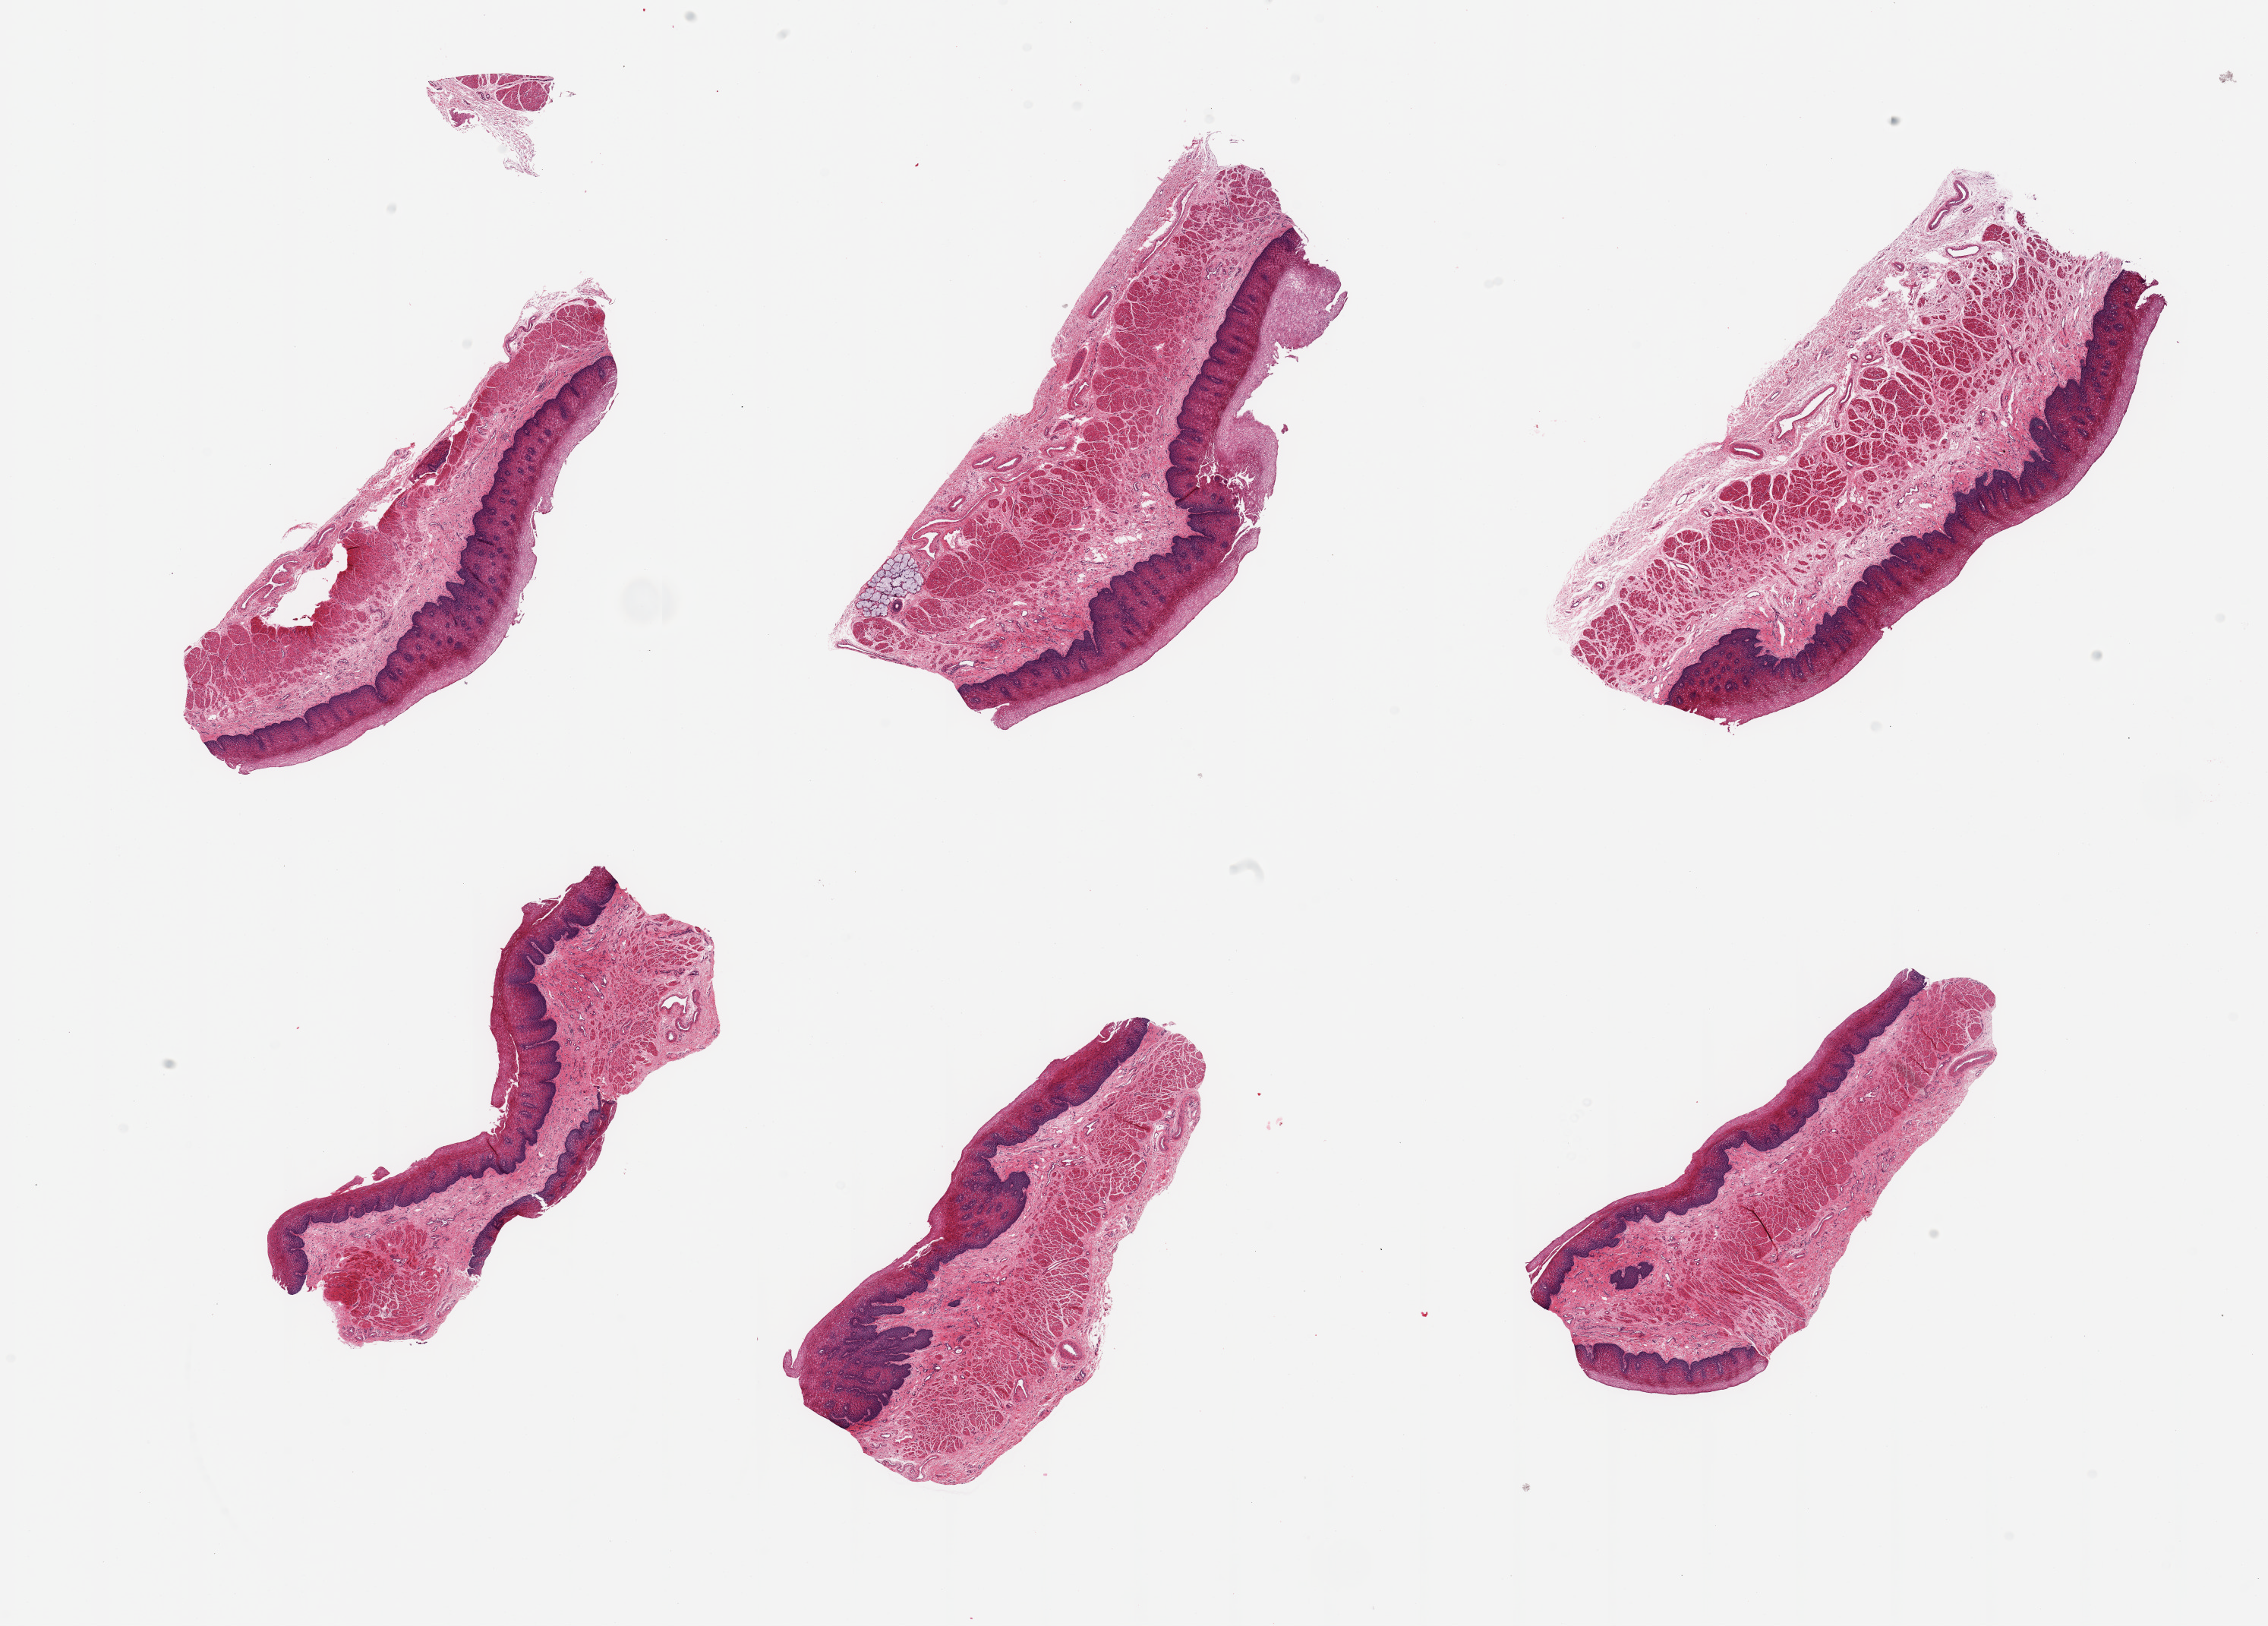
Whole-slide image, hematoxylin and eosin (H&E) stain, brightfield — low-resolution overview of the scanned area, about 23.6 x 16.9 mm (from a 20x scan); PAXgene-fixed paraffin-embedded (PFPE) section; sampled site (target tissue): esophageal mucous membrane; tissue donor sample.
Reviewer comment on this tissue sample: 6 pieces; target squamous mucosa and prominent muscularis mucosae.